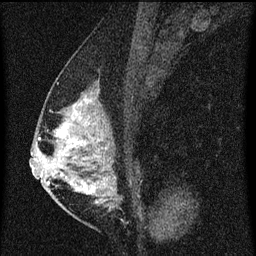
Breast MRI (dynamic contrast-enhanced), one sagittal slice. Dynamic contrast-enhanced series, image 2 of 3 at this slice position (ordered by acquisition). 1.5 T. TE 4.2 ms, TR 8 ms. 256 × 256 image matrix, field of view 180 × 180 mm. Female patient, age 47 years.
Outlined on this slice (semi-automatic segmentation, software-assisted and operator-edited):
- analysis volume of interest (the breast-tissue region the enhancement analysis was run in; not a lesion): box from (x=50, y=80) to (x=139, y=203) px
- tumour enhancement mask (voxels above the 70 % enhancement threshold inside the analysis volume of interest): (x=50, y=92)–(x=107, y=203)